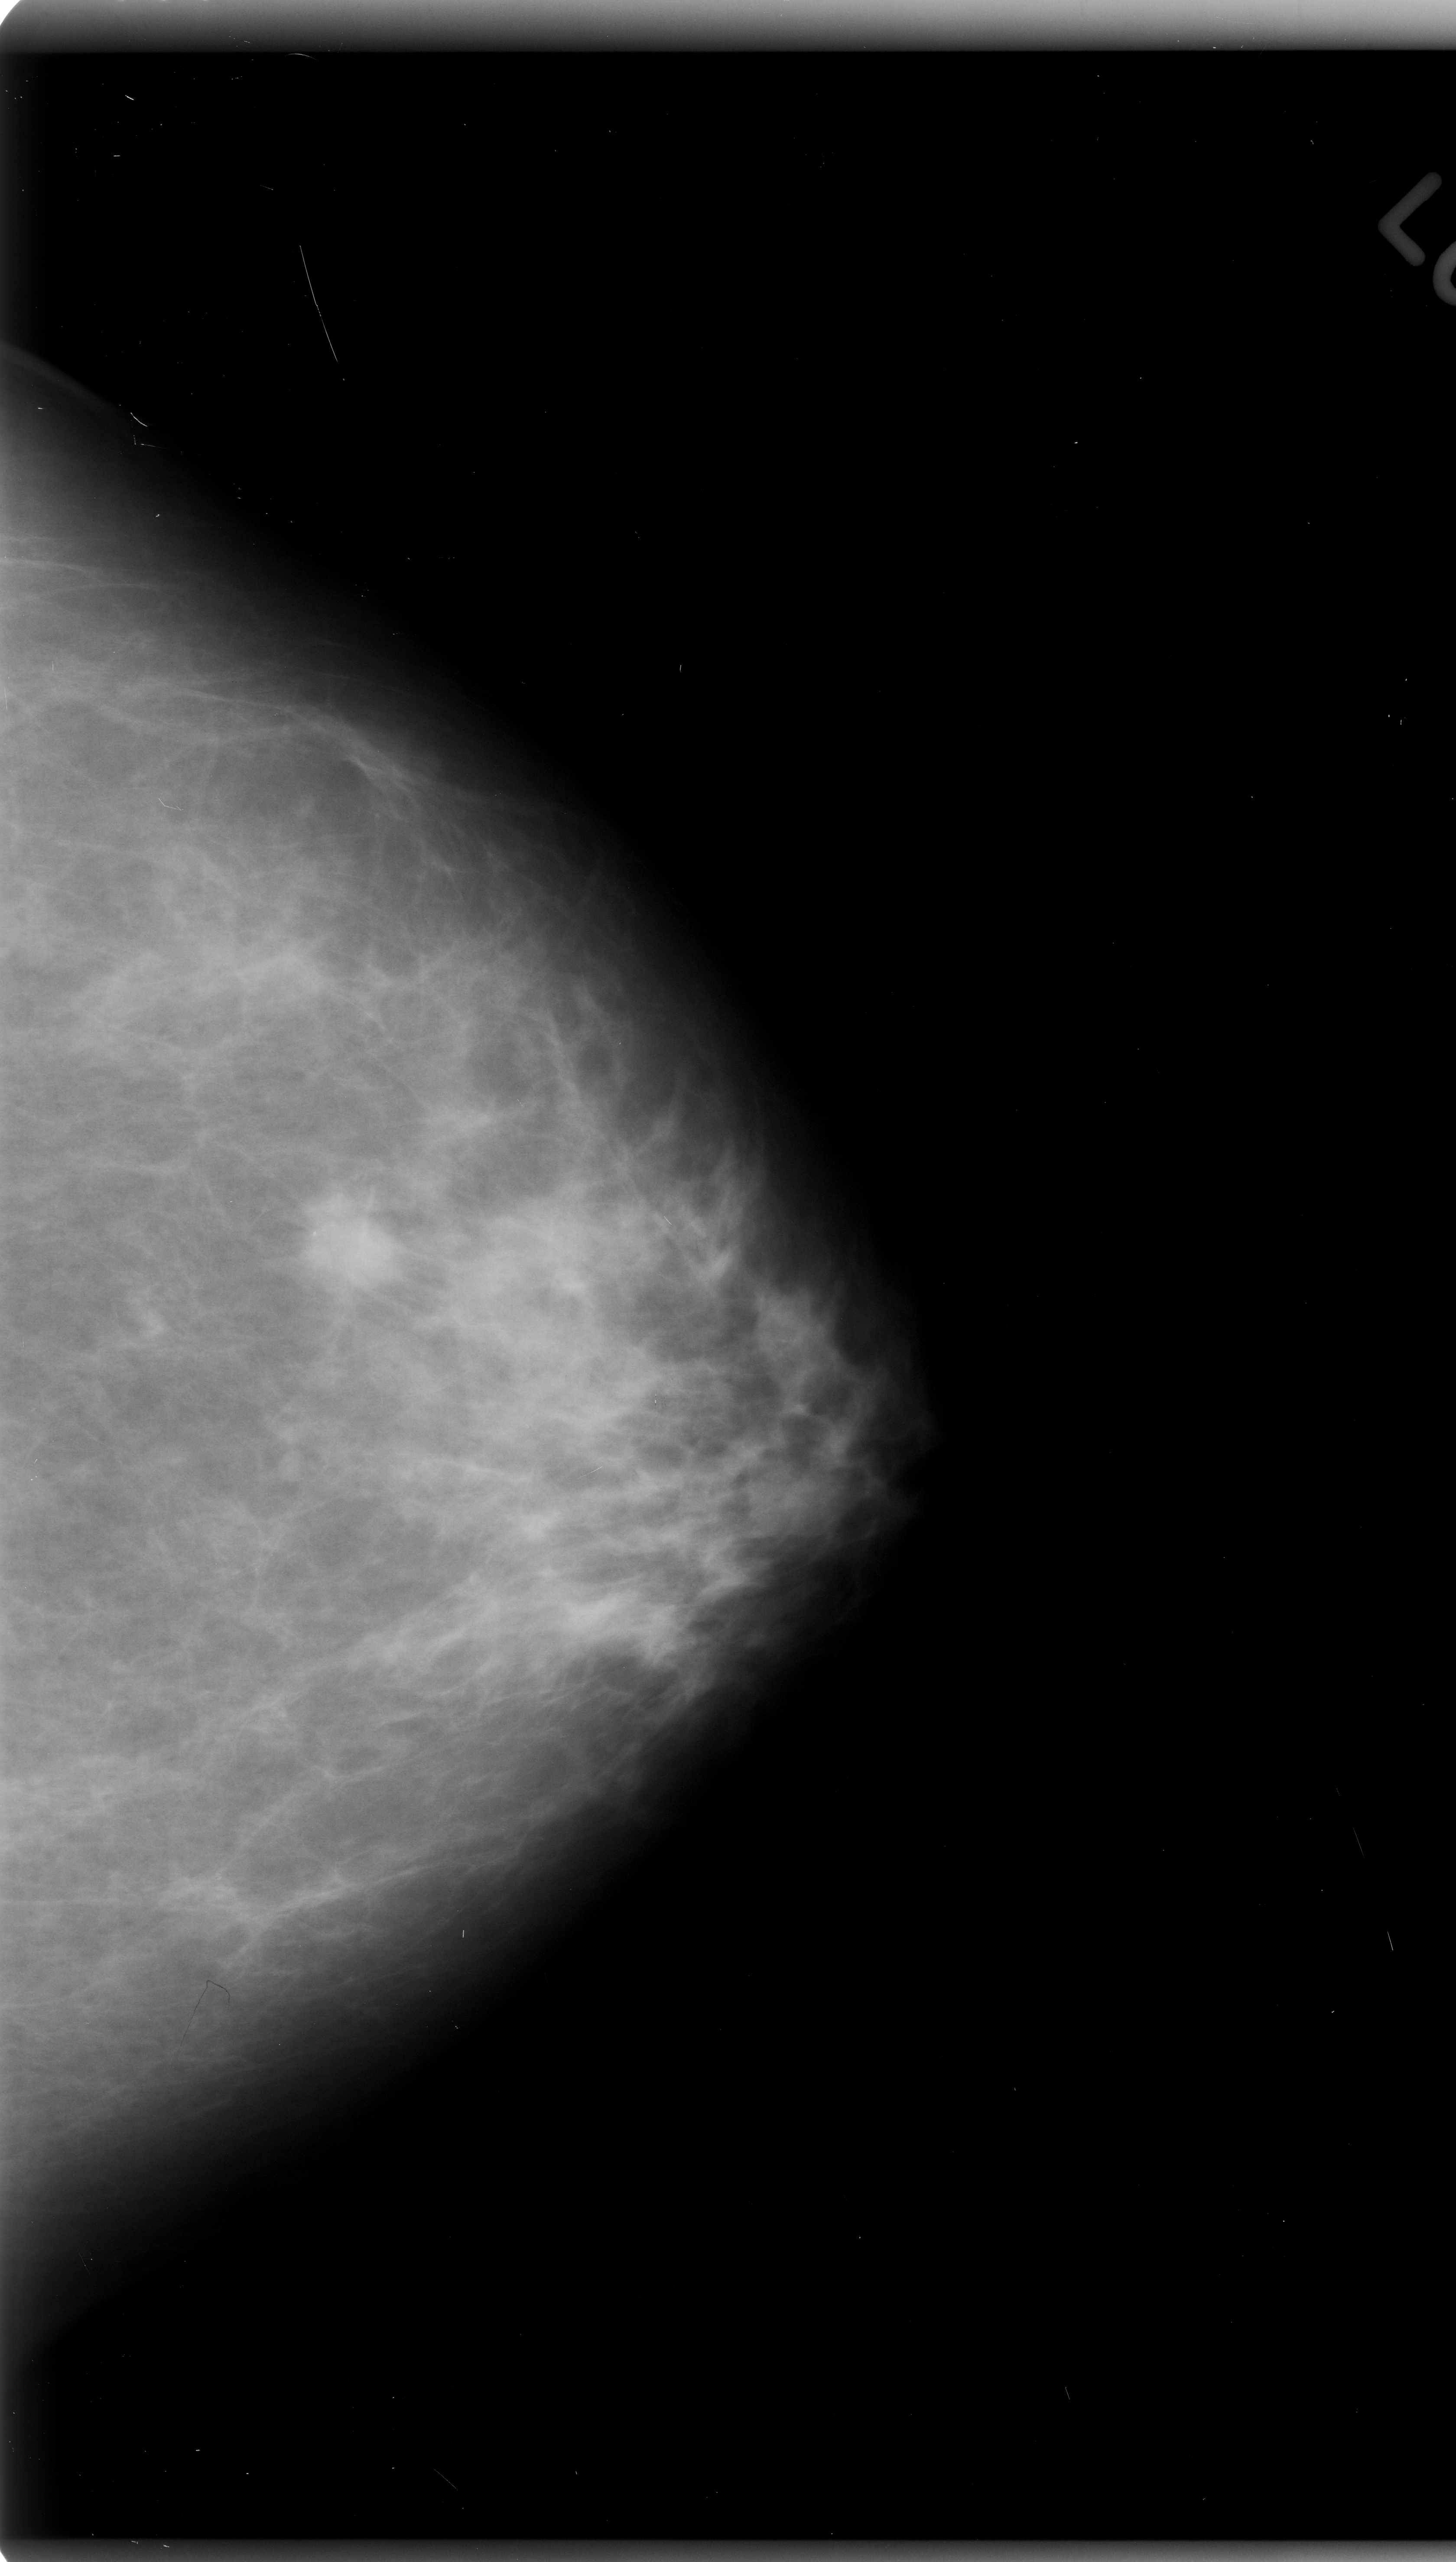
Mammogram (digitized film); left breast; CC view; BI-RADS breast density category 2 (scale 1–4); 1456 × 2562 image matrix.
Expert-marked regions of interest on this film, with their recorded descriptors:
- mass, shape oval, margins spiculated; BI-RADS assessment category 5; pathology (as recorded): malignant: bounding box <280,1178,426,1330> (left, top, right, bottom; pixels)